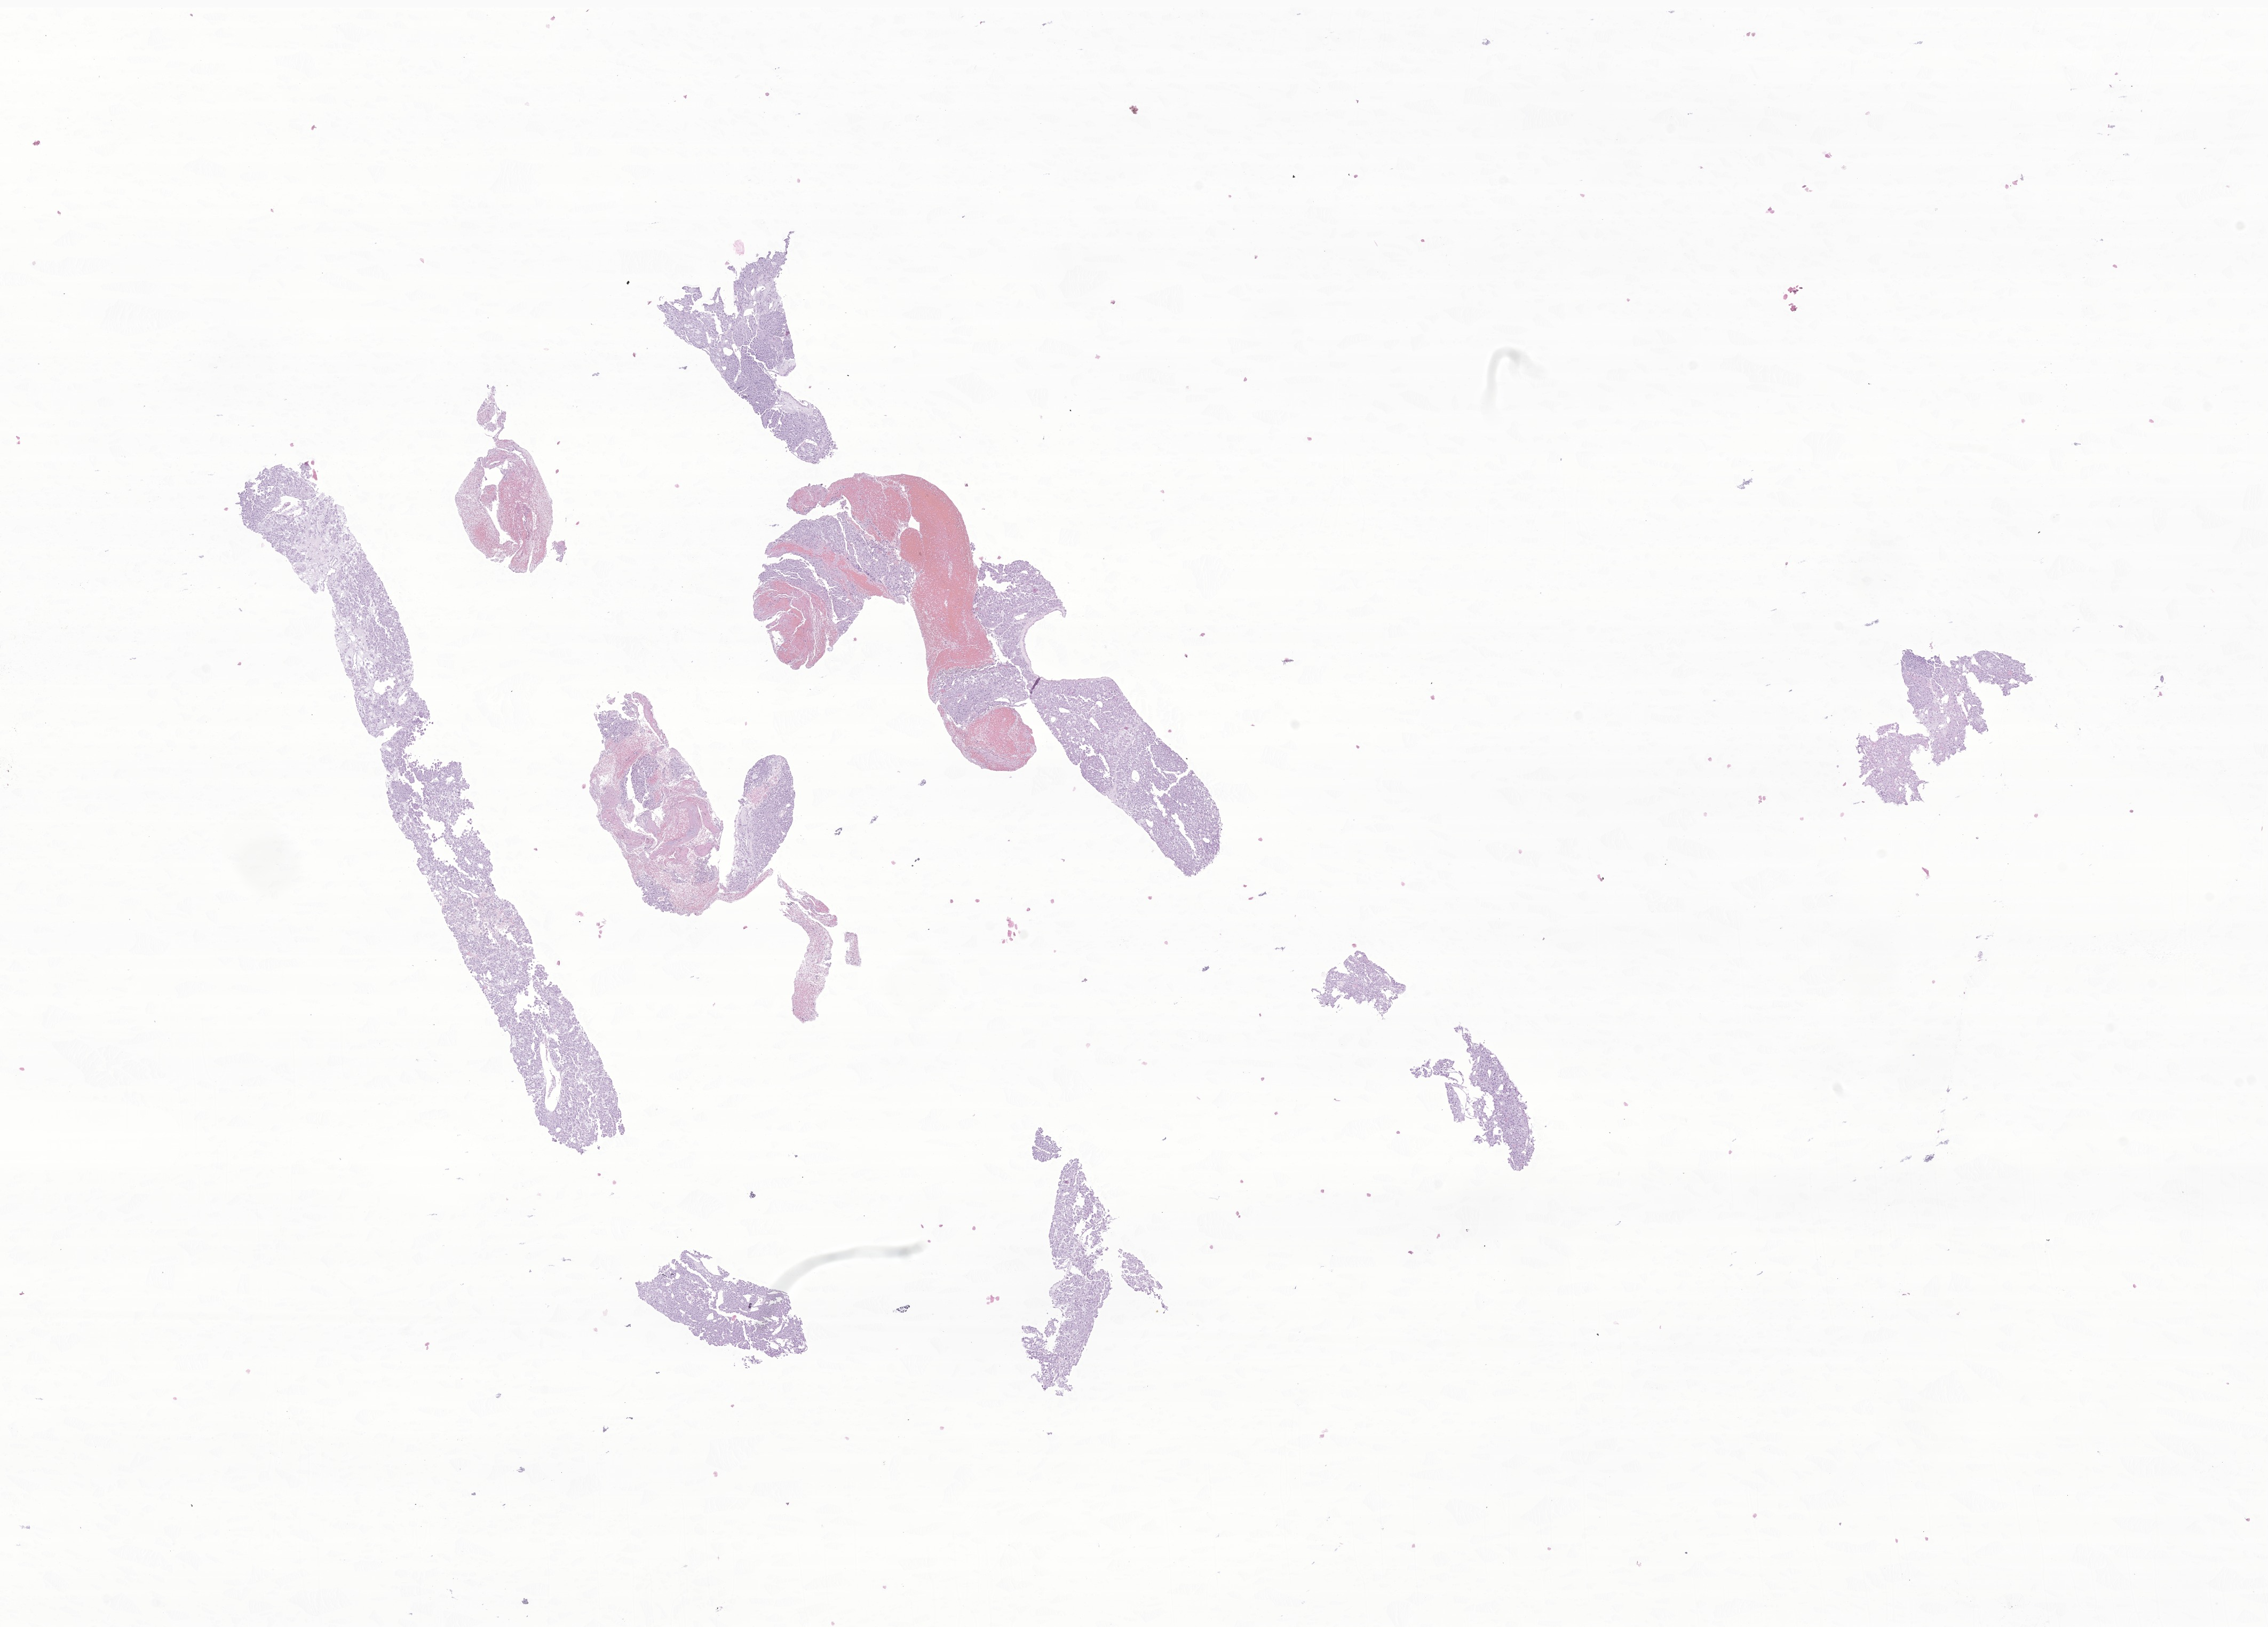
Digitized haematoxylin and eosin-stained section of tumor tissue from the soft tissue of lower extremity, low-resolution overview of the scanned area, about 17.9 x 12.9 mm. Formalin-fixed, paraffin-embedded (FFPE) tissue. Male patient, age 200 months (16 years 8 months).
* diagnosis: Alveolar soft part sarcoma